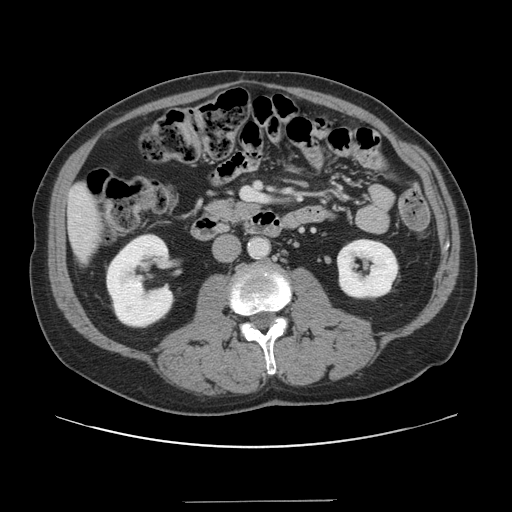
Contrast-enhanced abdominal CT, one axial slice. Position 42 of 151 along the scan axis. 120 kVp. Intravenous contrast given. Soft-tissue window (W 400 / L 40 HU). 512 × 512 image matrix, field of view 399 × 399 mm. Male patient, age 63 years. From the clinical record (not read from this slice): diagnosis: colorectal cancer liver metastases, imaged before liver resection; multiple liver metastases: no.
Structures marked on this image (expert manual segmentation):
- liver: box from (x=69, y=185) to (x=102, y=259) px
- planned liver remnant (the part of the liver to remain after resection): (x=69, y=185)–(x=102, y=260)
- portal vein (with intrahepatic branches): (x=243, y=189)–(x=265, y=201)